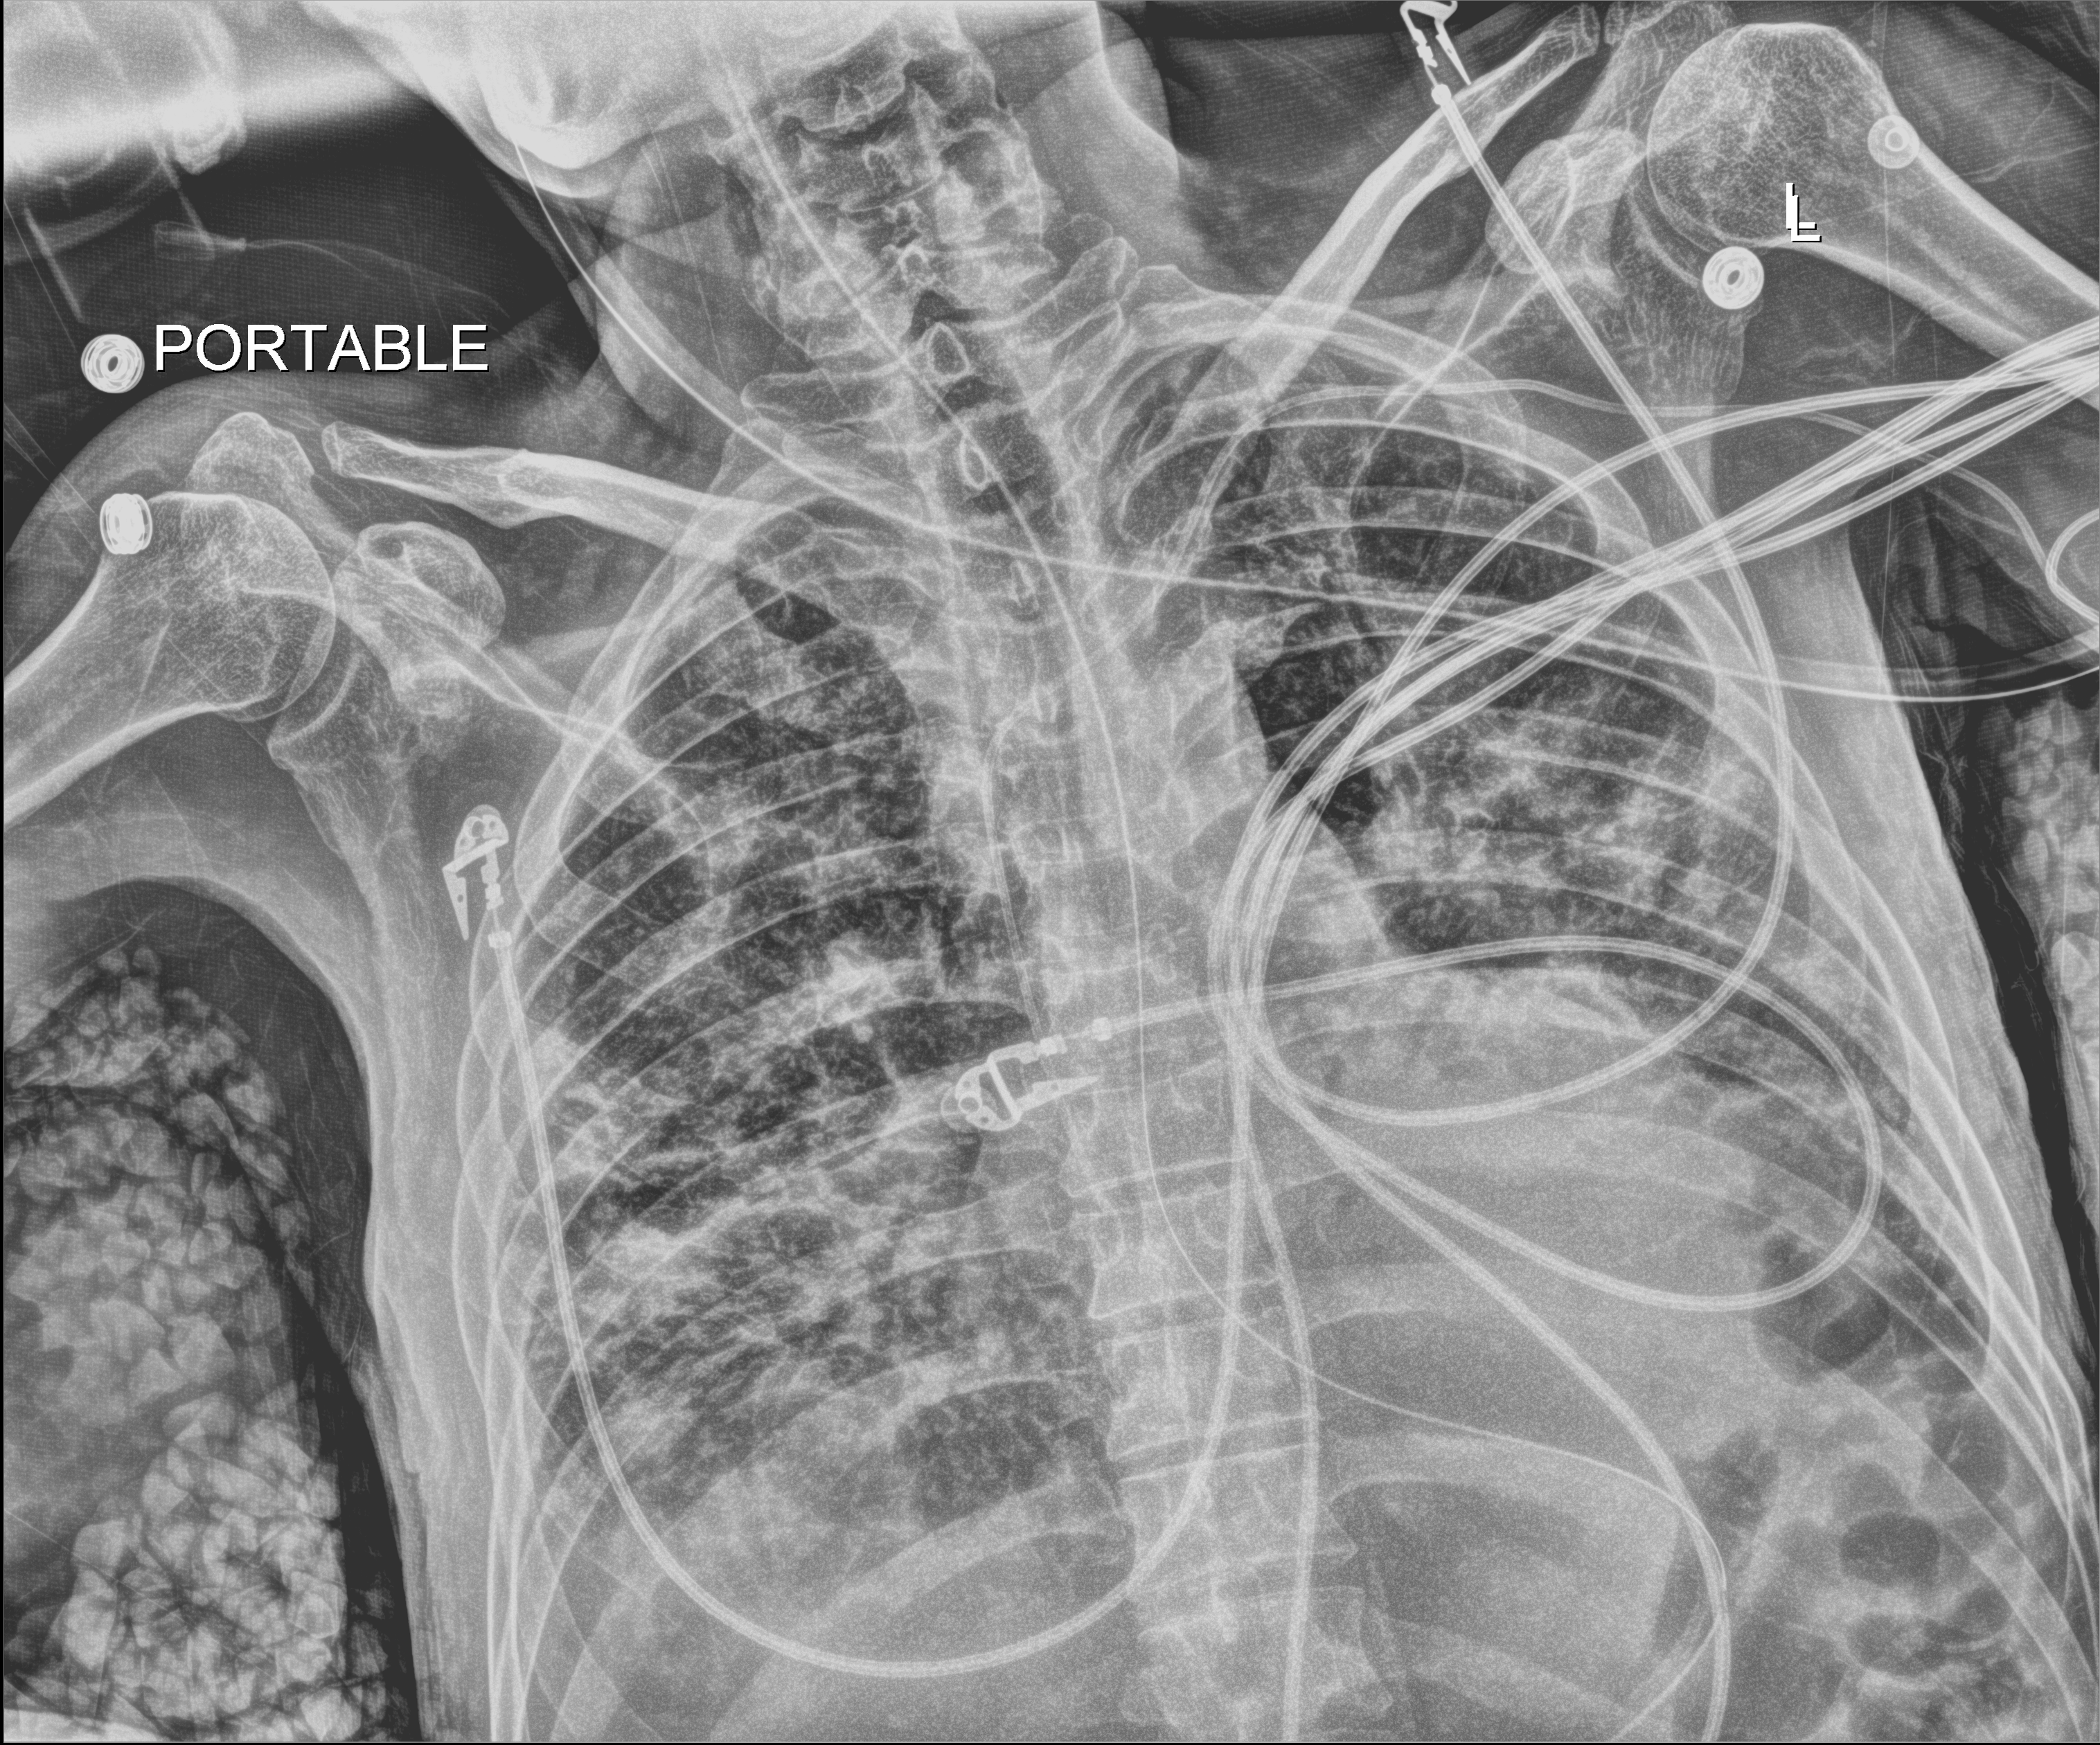
Chest radiograph (digital radiography). Male patient hospitalised with COVID-19, age 18–59 years.
From the hospital-stay record, not from the radiograph (when in the stay this image was taken is not recorded): COPD (admission record): no; admitted to intensive care during this hospital stay: yes.